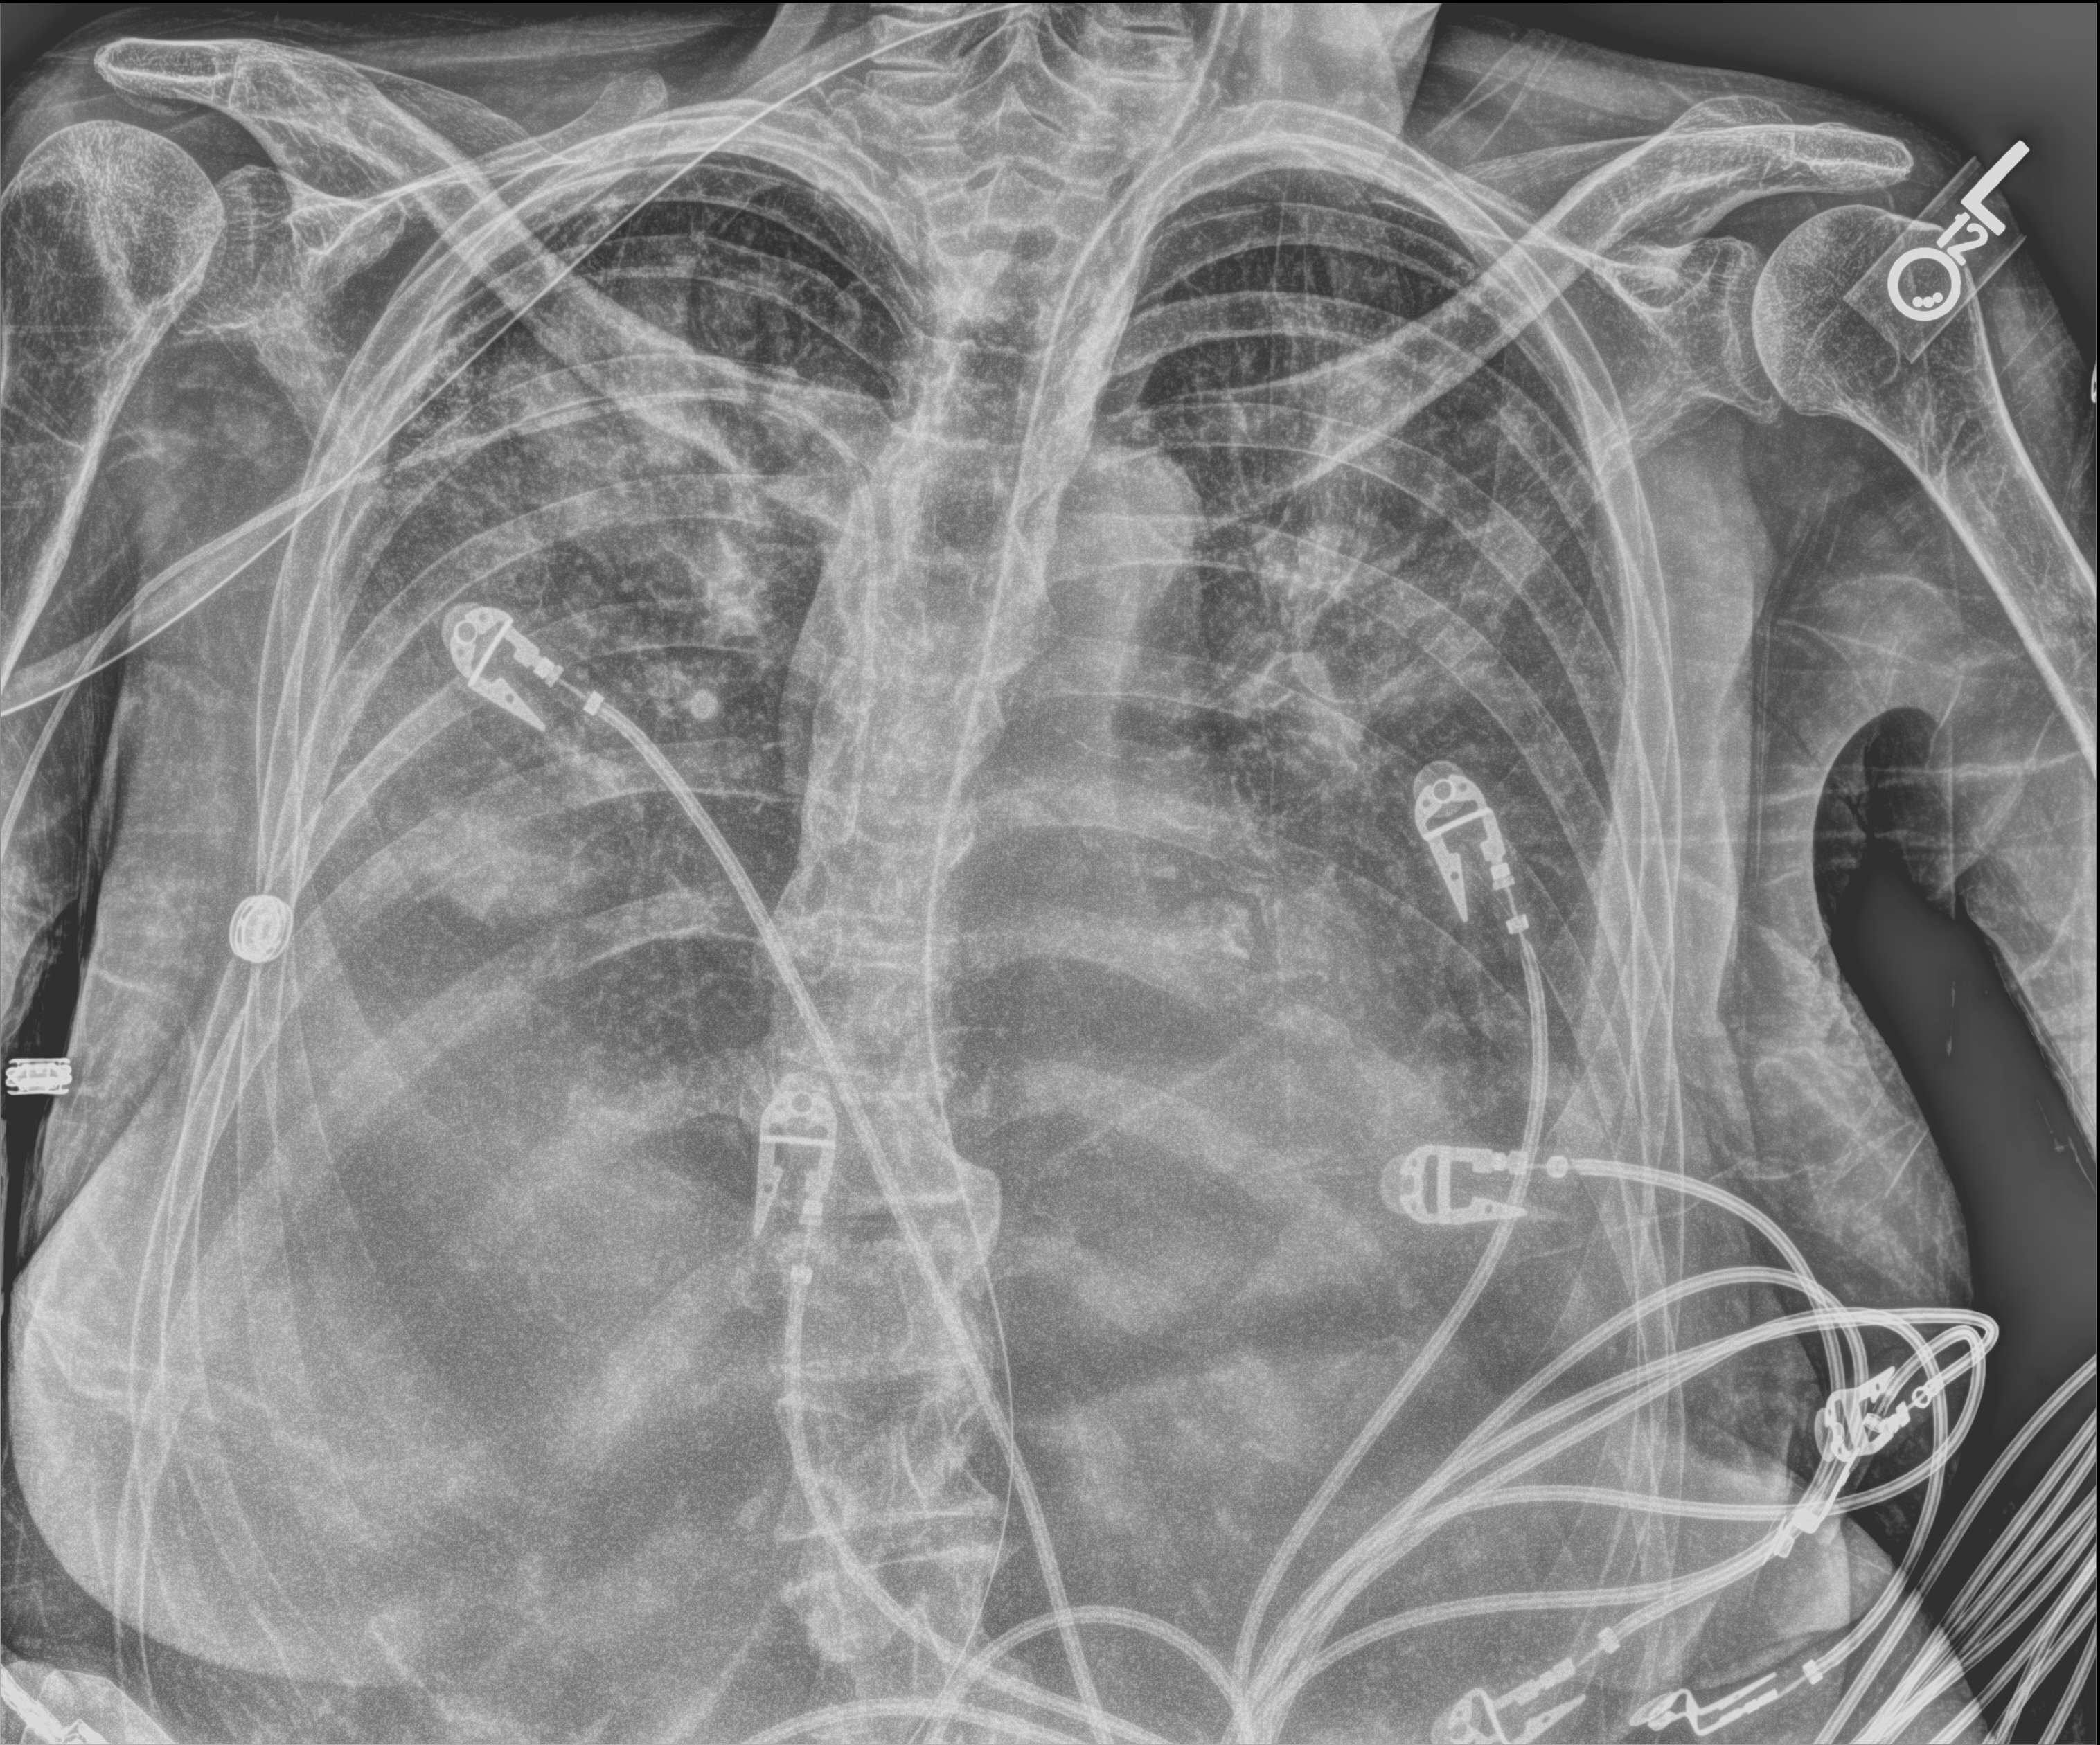
Chest X-ray (portable), anteroposterior (AP) projection. Female patient hospitalised with COVID-19, age 60–74 years.
From the hospital-stay record, not from the radiograph (when in the stay this image was taken is not recorded):
- mechanically ventilated during this hospital stay: no
- length of hospital stay: 10 days
- admitted to intensive care during this hospital stay: yes